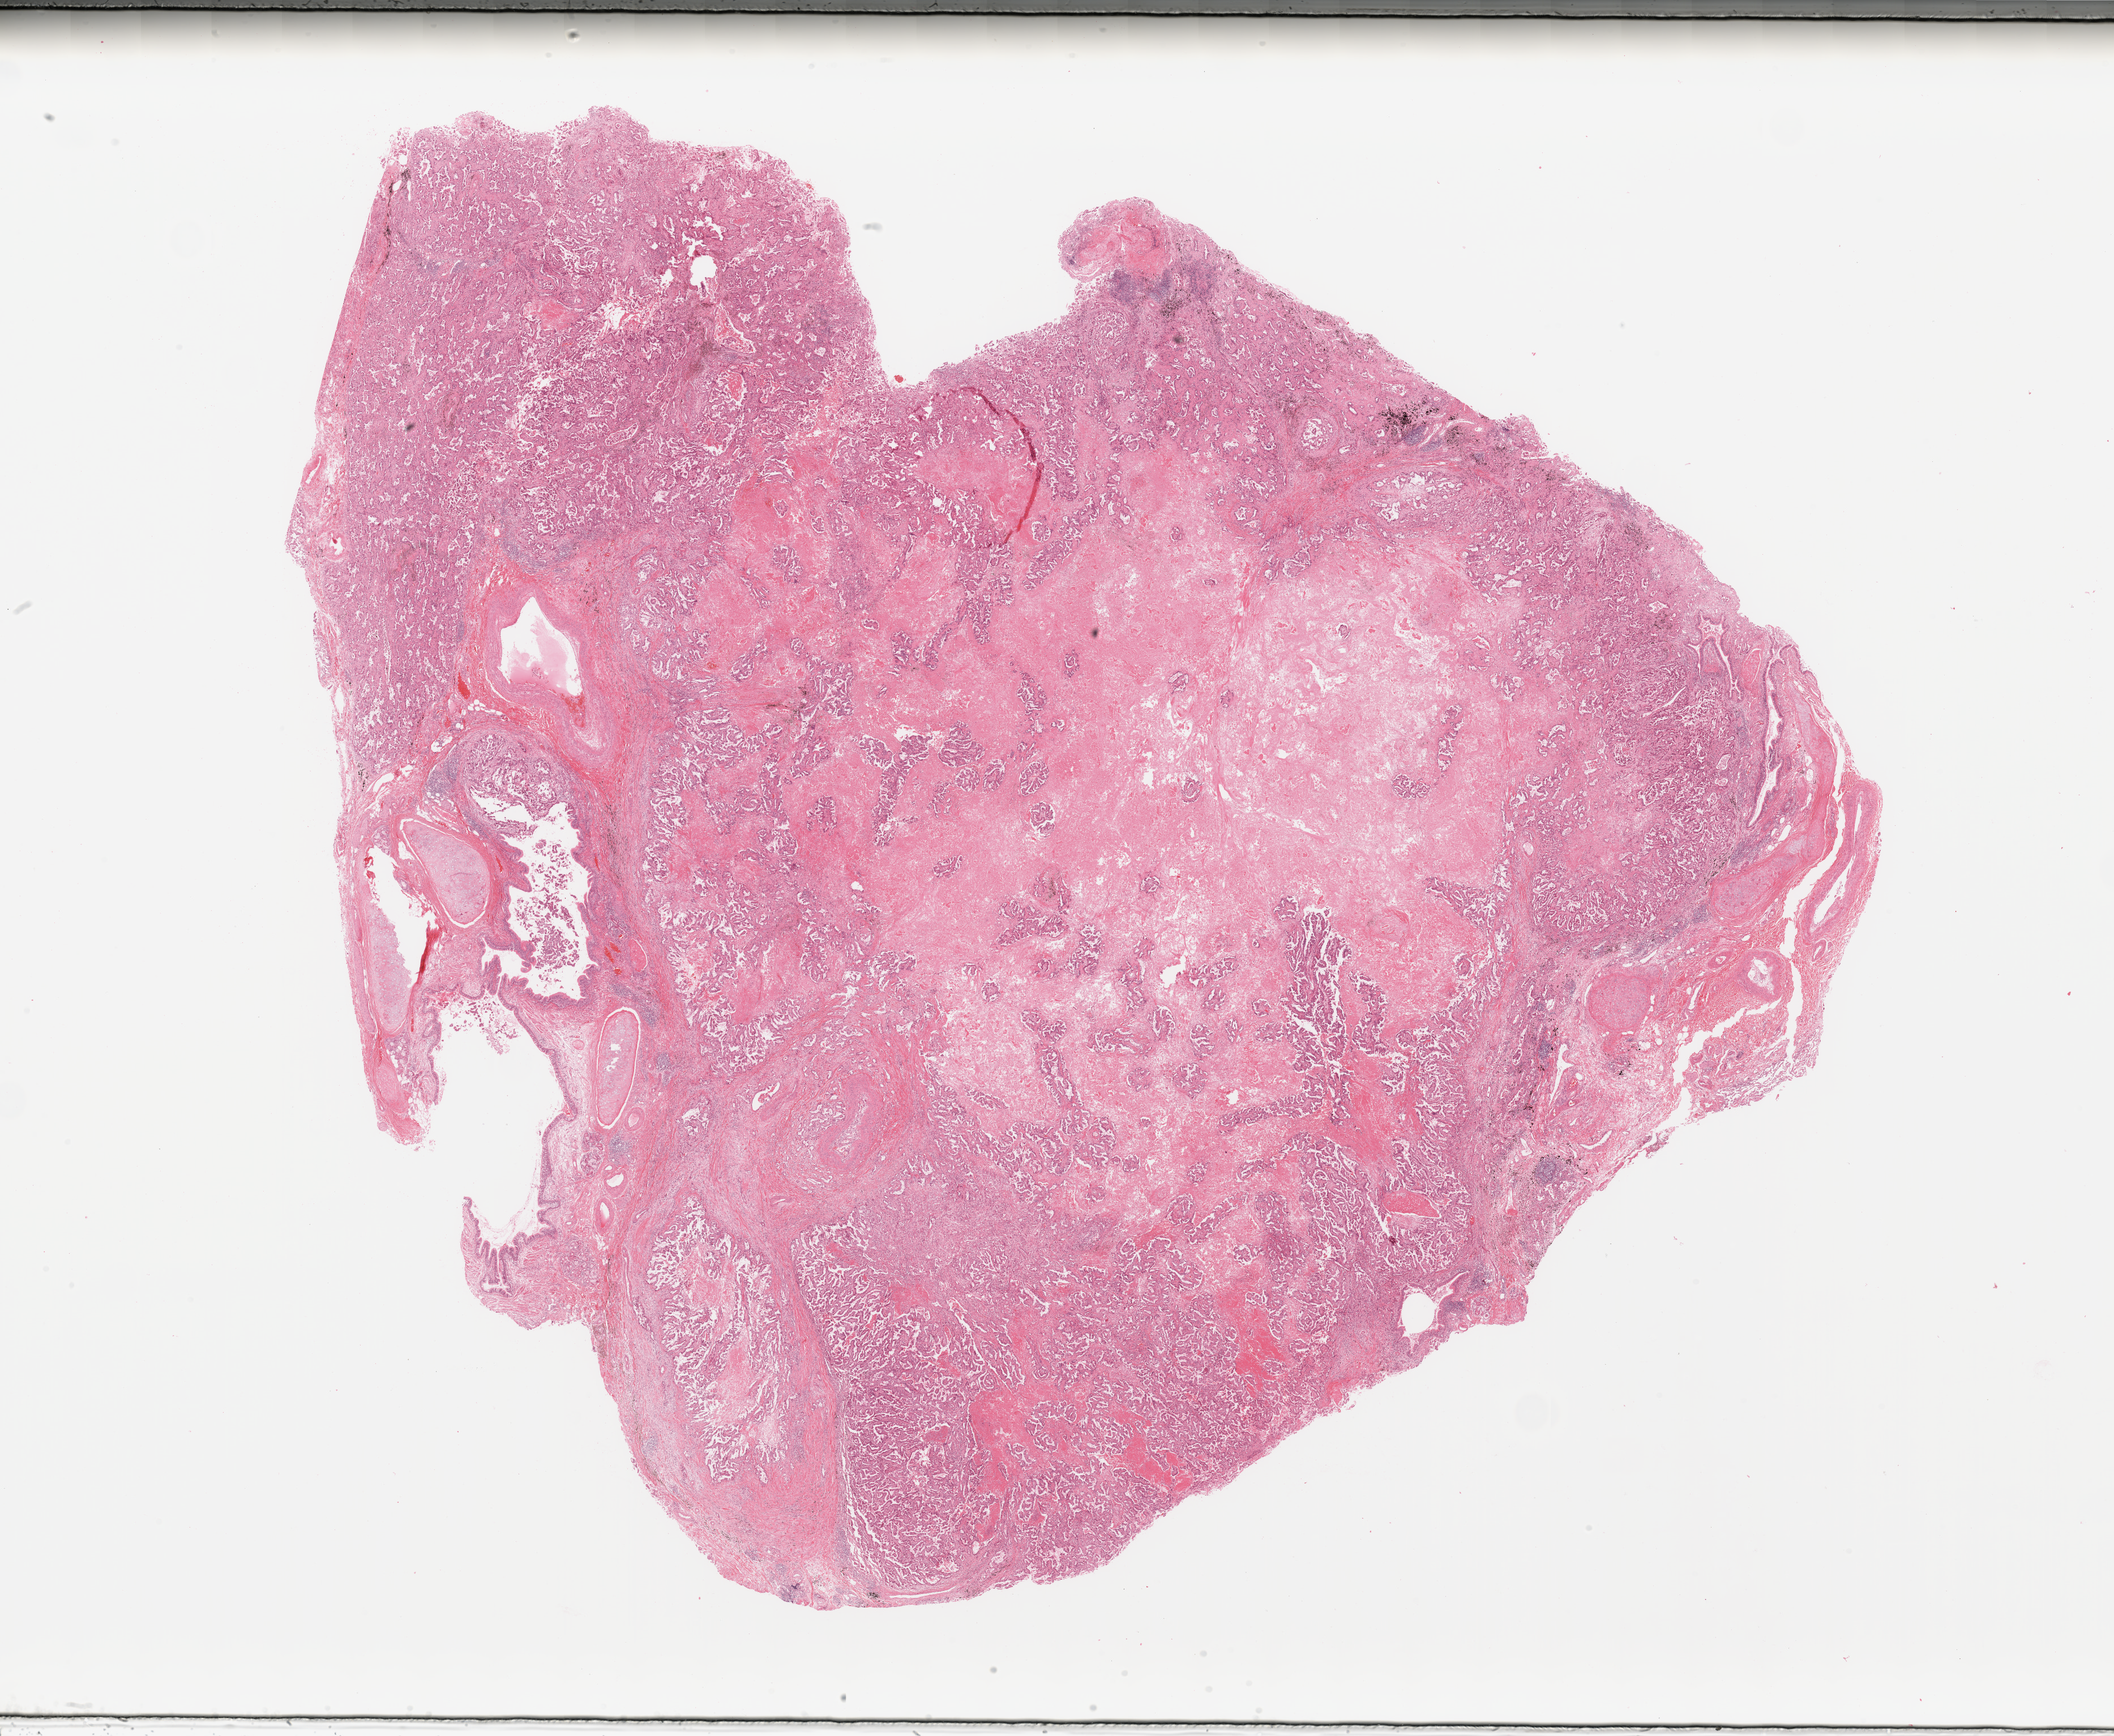
Digitized H&E tissue section (whole slide), shown as a low-resolution overview of the whole scanned area (about 29.5 x 24.3 mm, slide scanned at 20x); lung, tumour tissue. 69-year-old female patient.
Diagnosis: Adenocarcinoma, NOS.